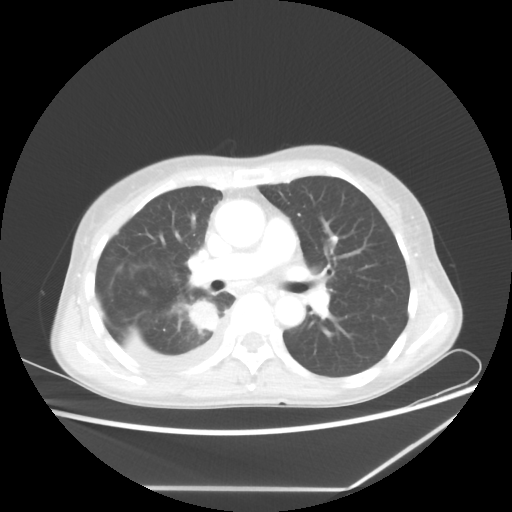
Chest CT, one axial slice. Slice 34 of 60 in the series (ordered by position). Reconstruction kernel STANDARD. 80 kVp. Lung window (W 1500 / L -600 HU). 5 mm slice thickness. 512 × 512 image matrix, field of view 364 × 364 mm. Female patient, age 59 years. Case-level facts recorded for this patient, not image findings: clinical TNM (as recorded): T1c N1 M1.
Outlined on this slice (rectangle marked by the reading radiologist):
- lung tumour (recorded histology: adenocarcinoma): bounding box <184,298,220,333> (left, top, right, bottom; pixels)